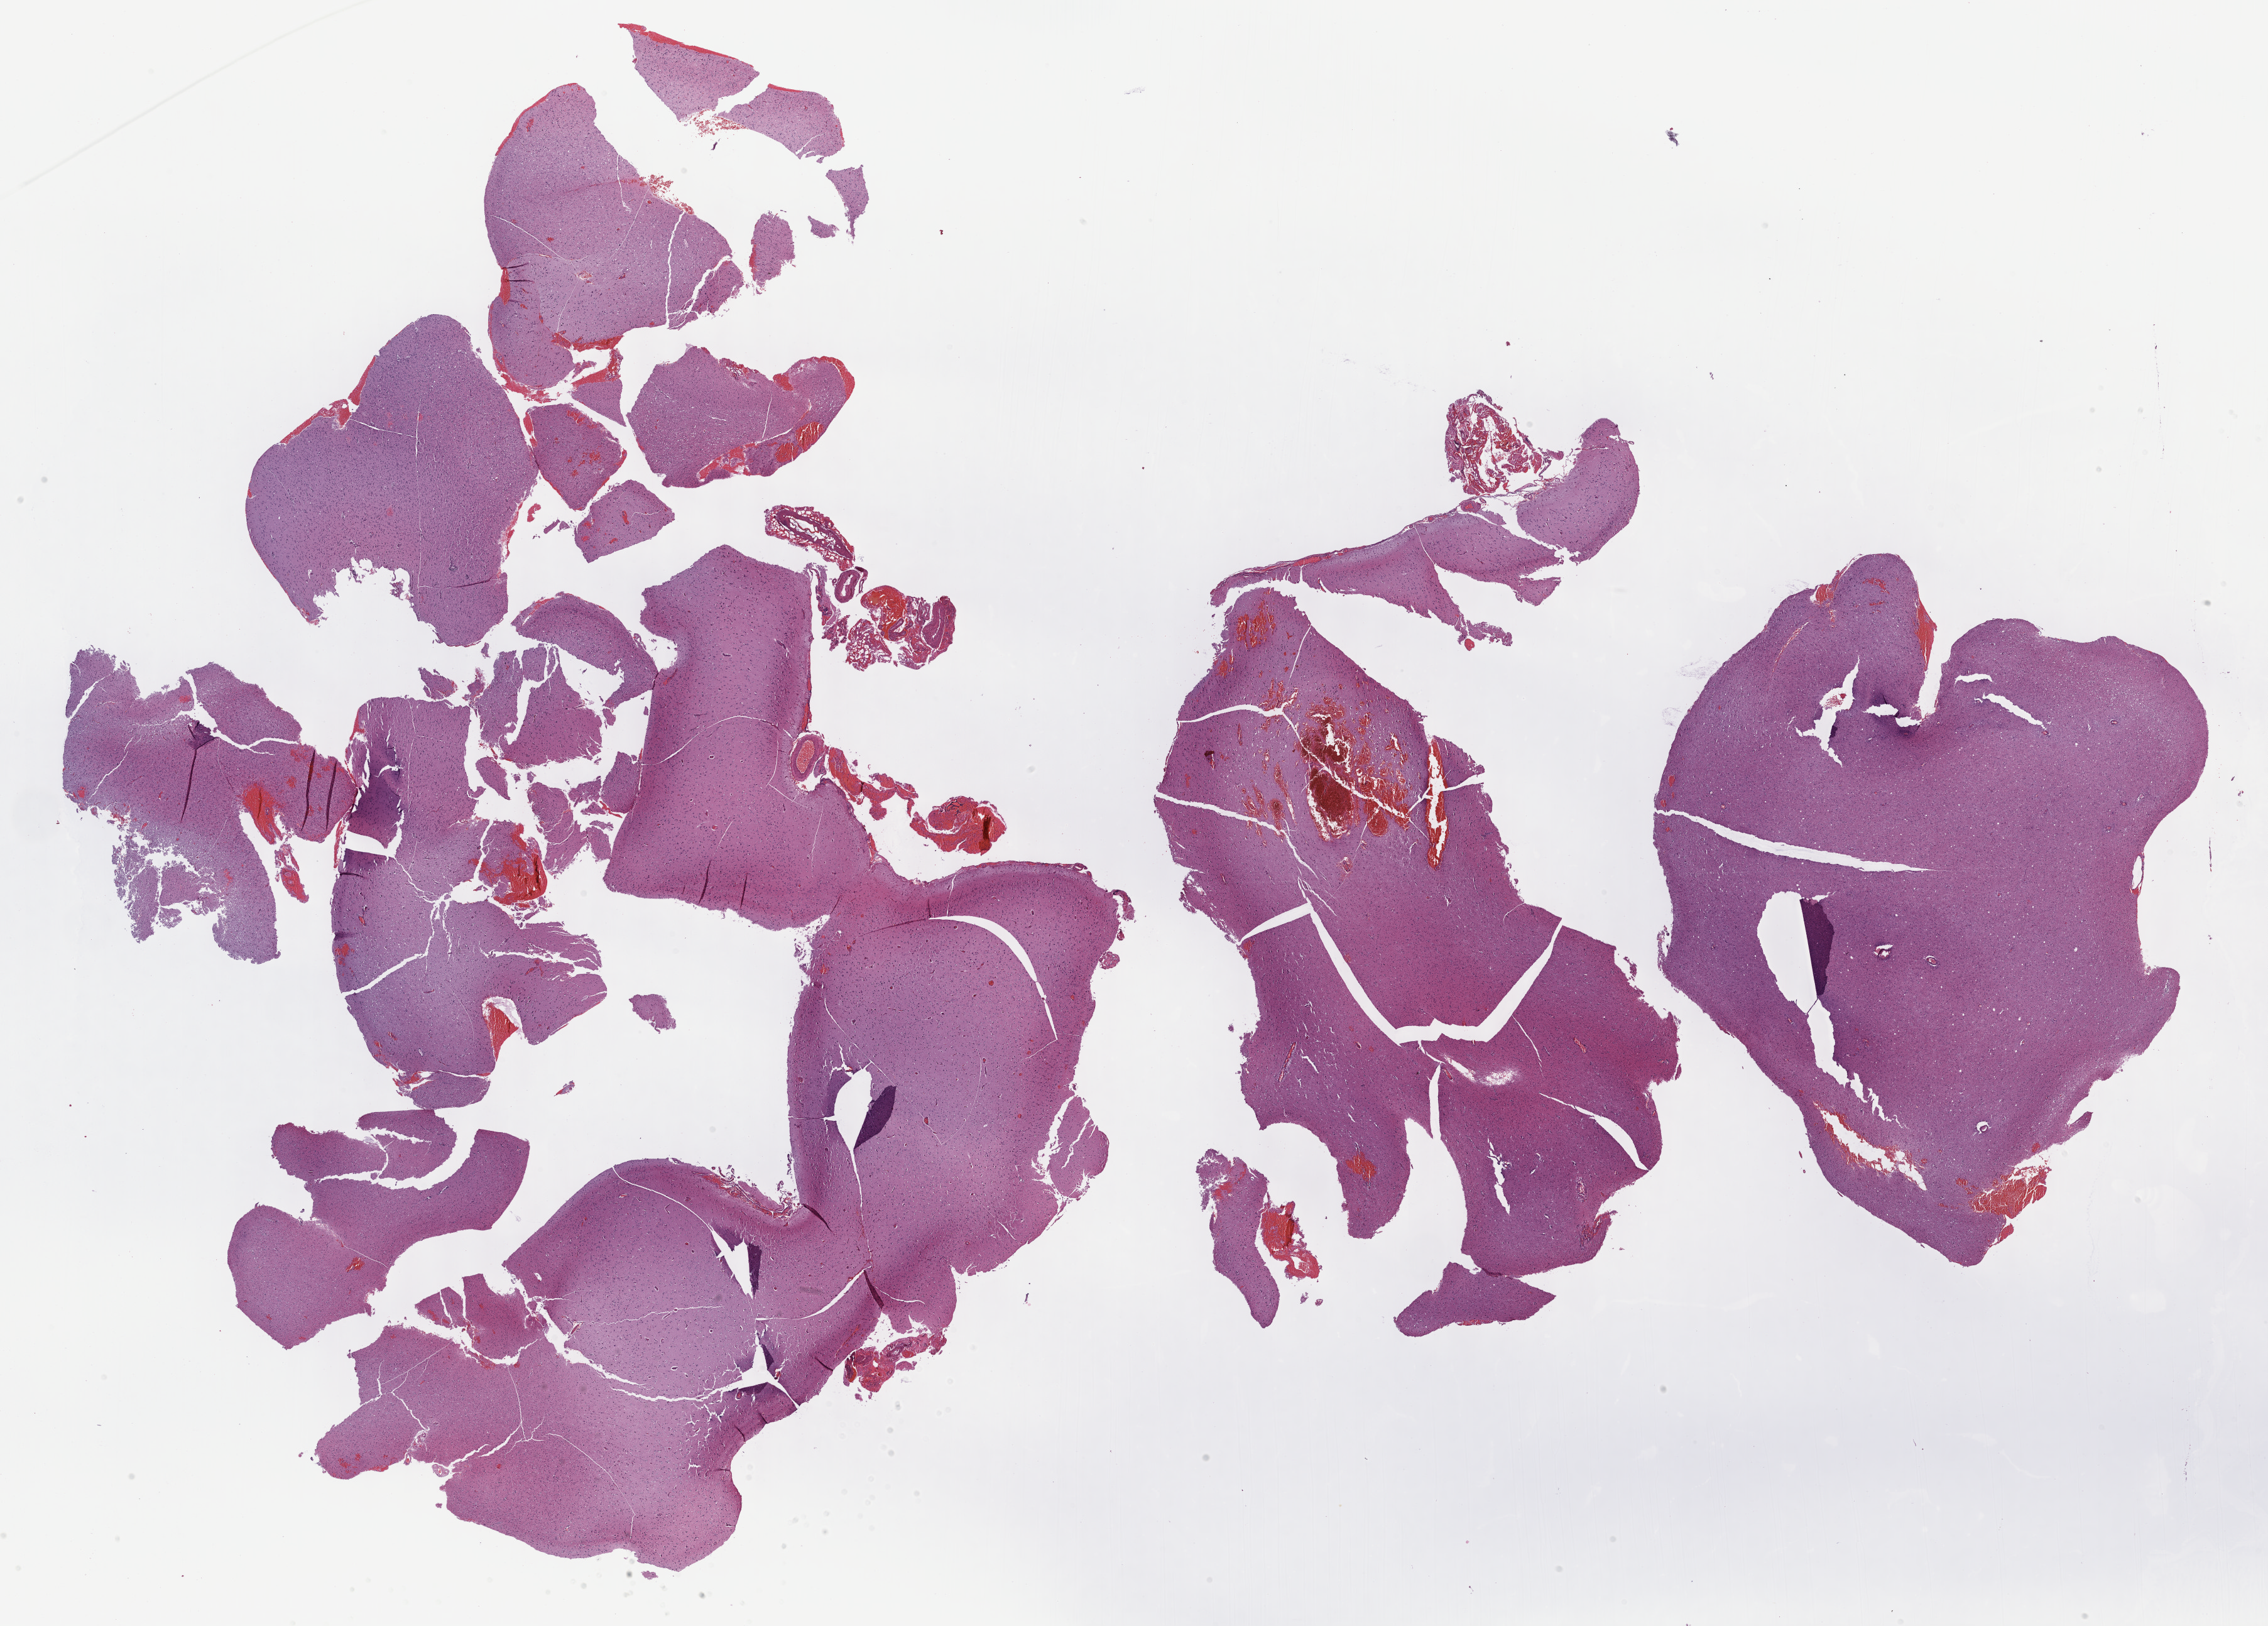
Digitized Hematoxylin and eosin (H&E) stained tissue section (whole slide) — a low-resolution overview of the entire scanned area, about 29.2 x 20.9 mm (from a 40x scan); formalin-fixed paraffin-embedded (FFPE) diagnostic section; brain, primary tumour sample. Patient: male, age at initial diagnosis 58 years. Histologic grade: G3 (poorly differentiated).
Laterality: right. Pathologic diagnosis: Astrocytoma, anaplastic (cerebrum).